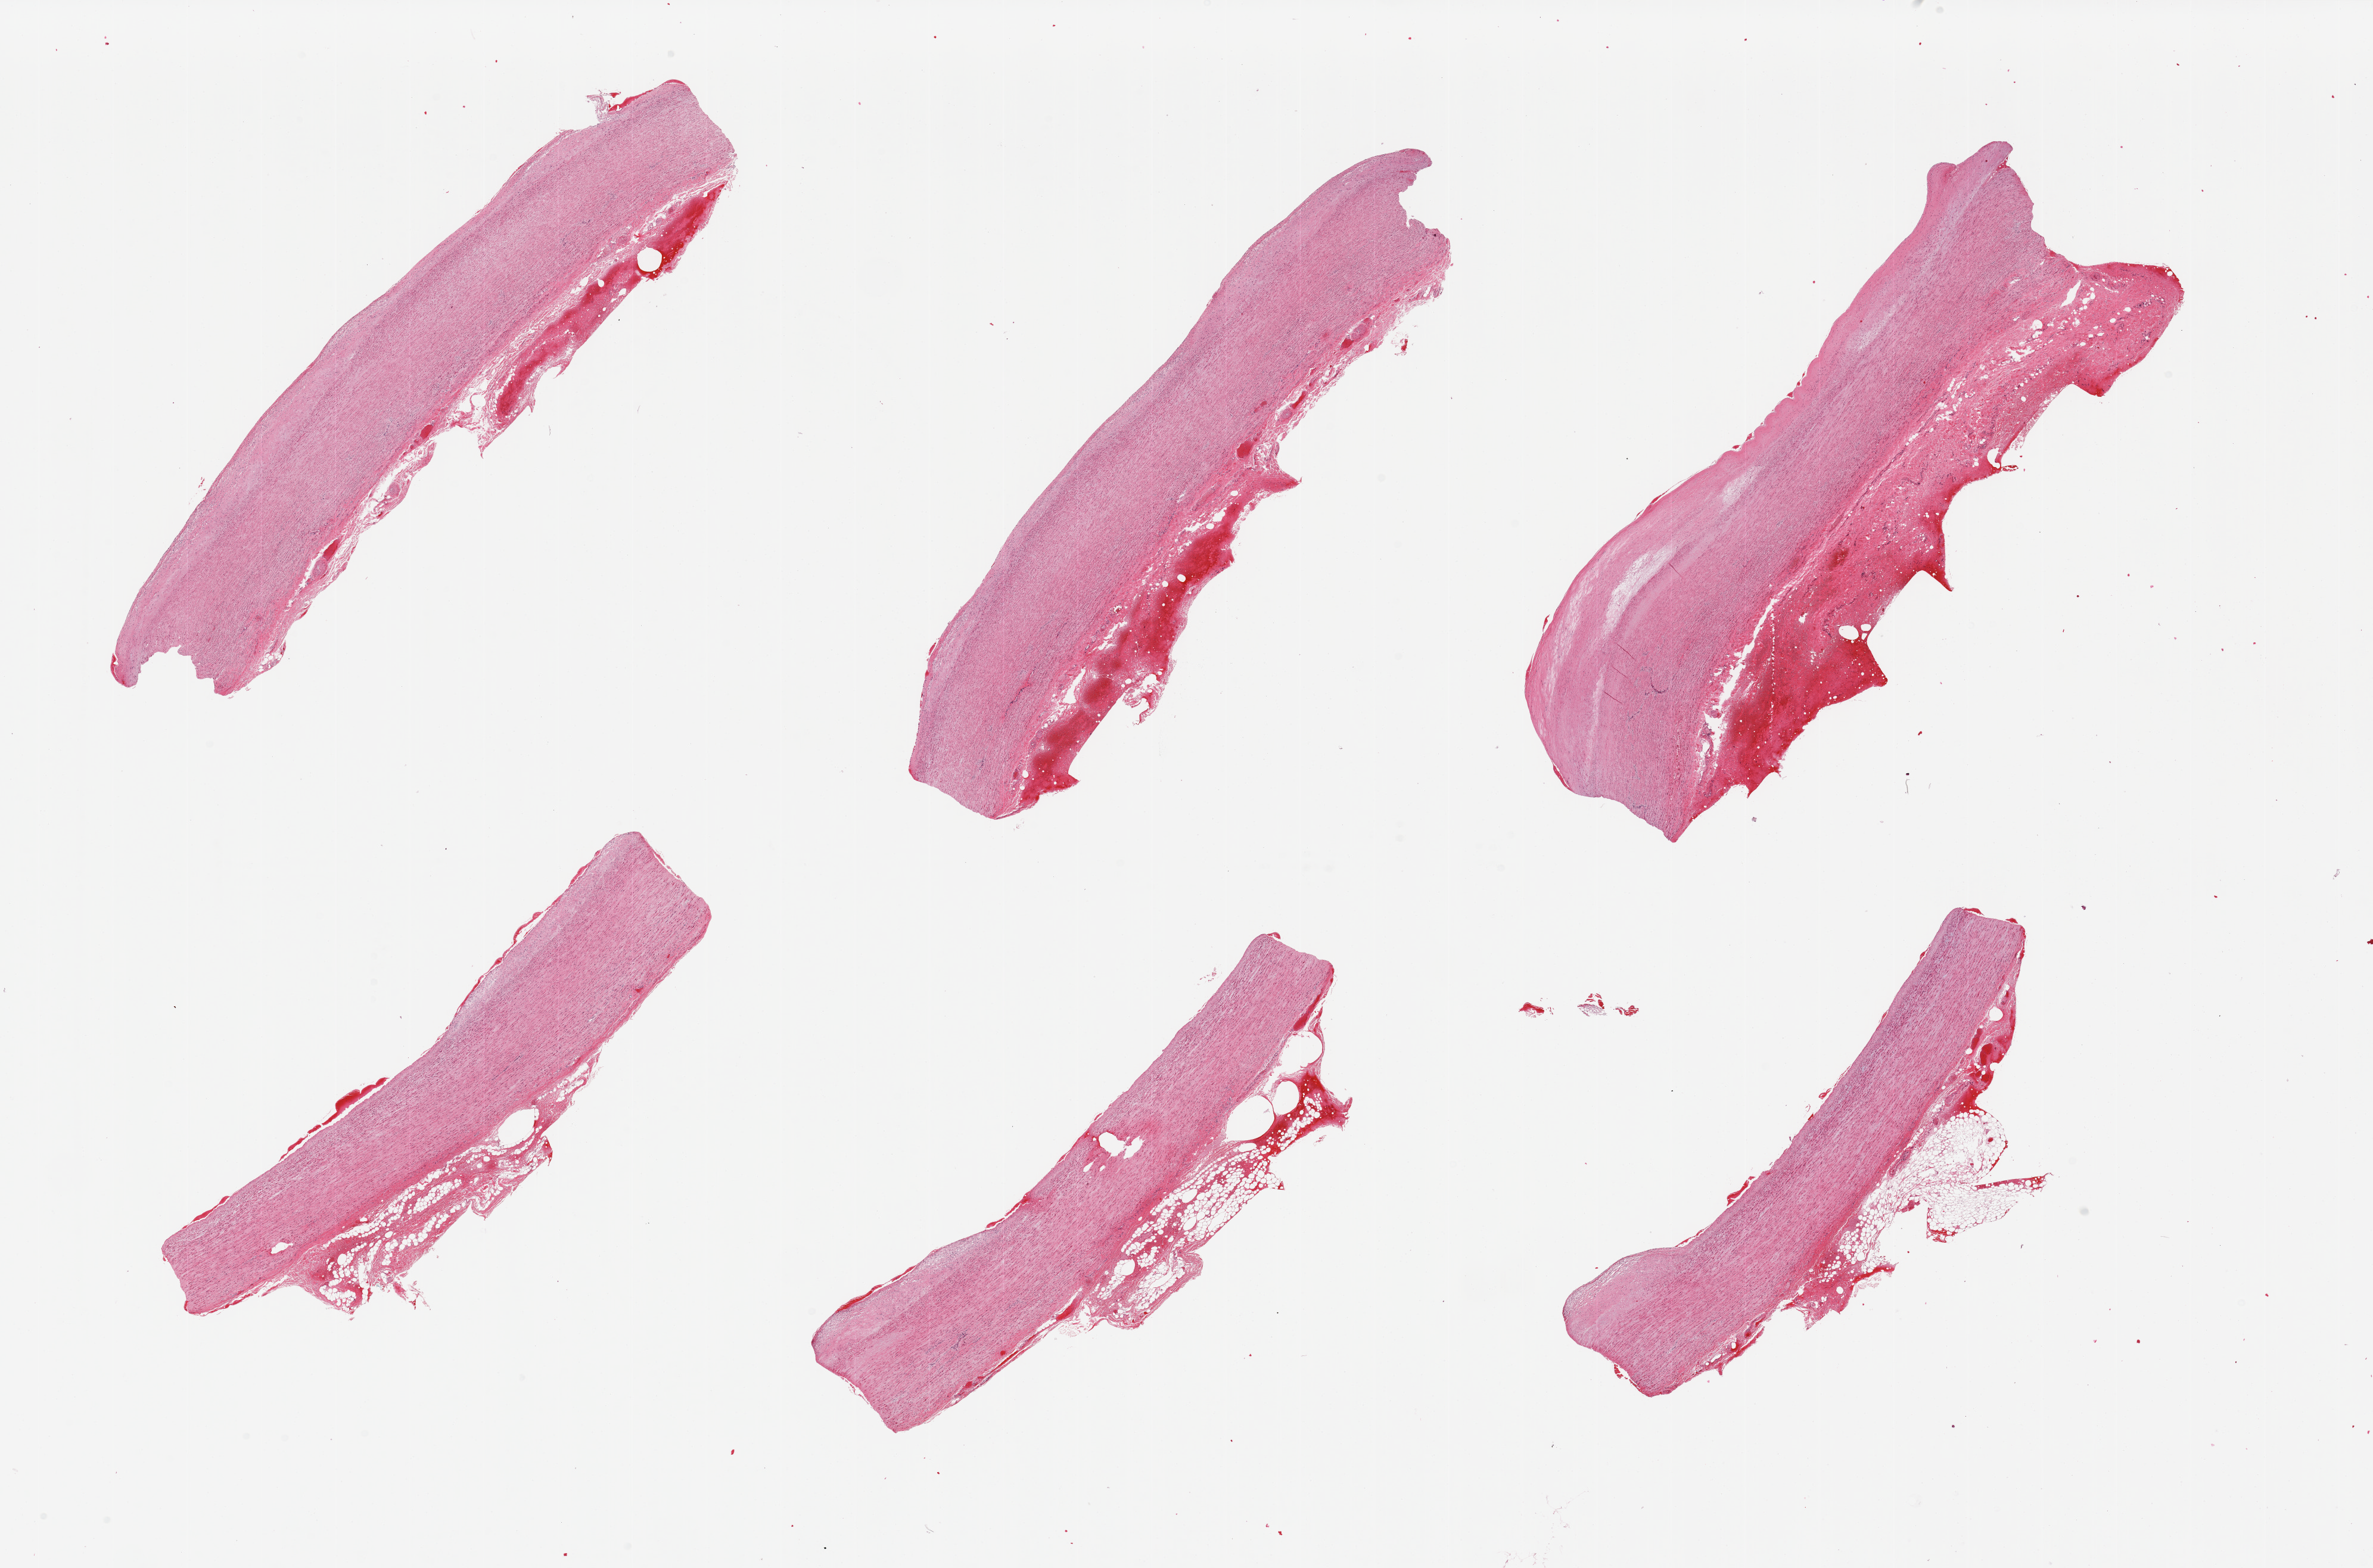
Whole-slide image, haematoxylin and eosin stain, brightfield, shown as a low-resolution overview of the whole scanned area (about 31.5 x 20.8 mm), PAXgene-fixed paraffin-embedded (PFPE) section, section of aorta (target tissue), tissue donor sample. Female donor.
* reviewer comment on this tissue sample: 6 pieces. adventitial hemorrhage in 3 pieces, up to 1.7mm thick